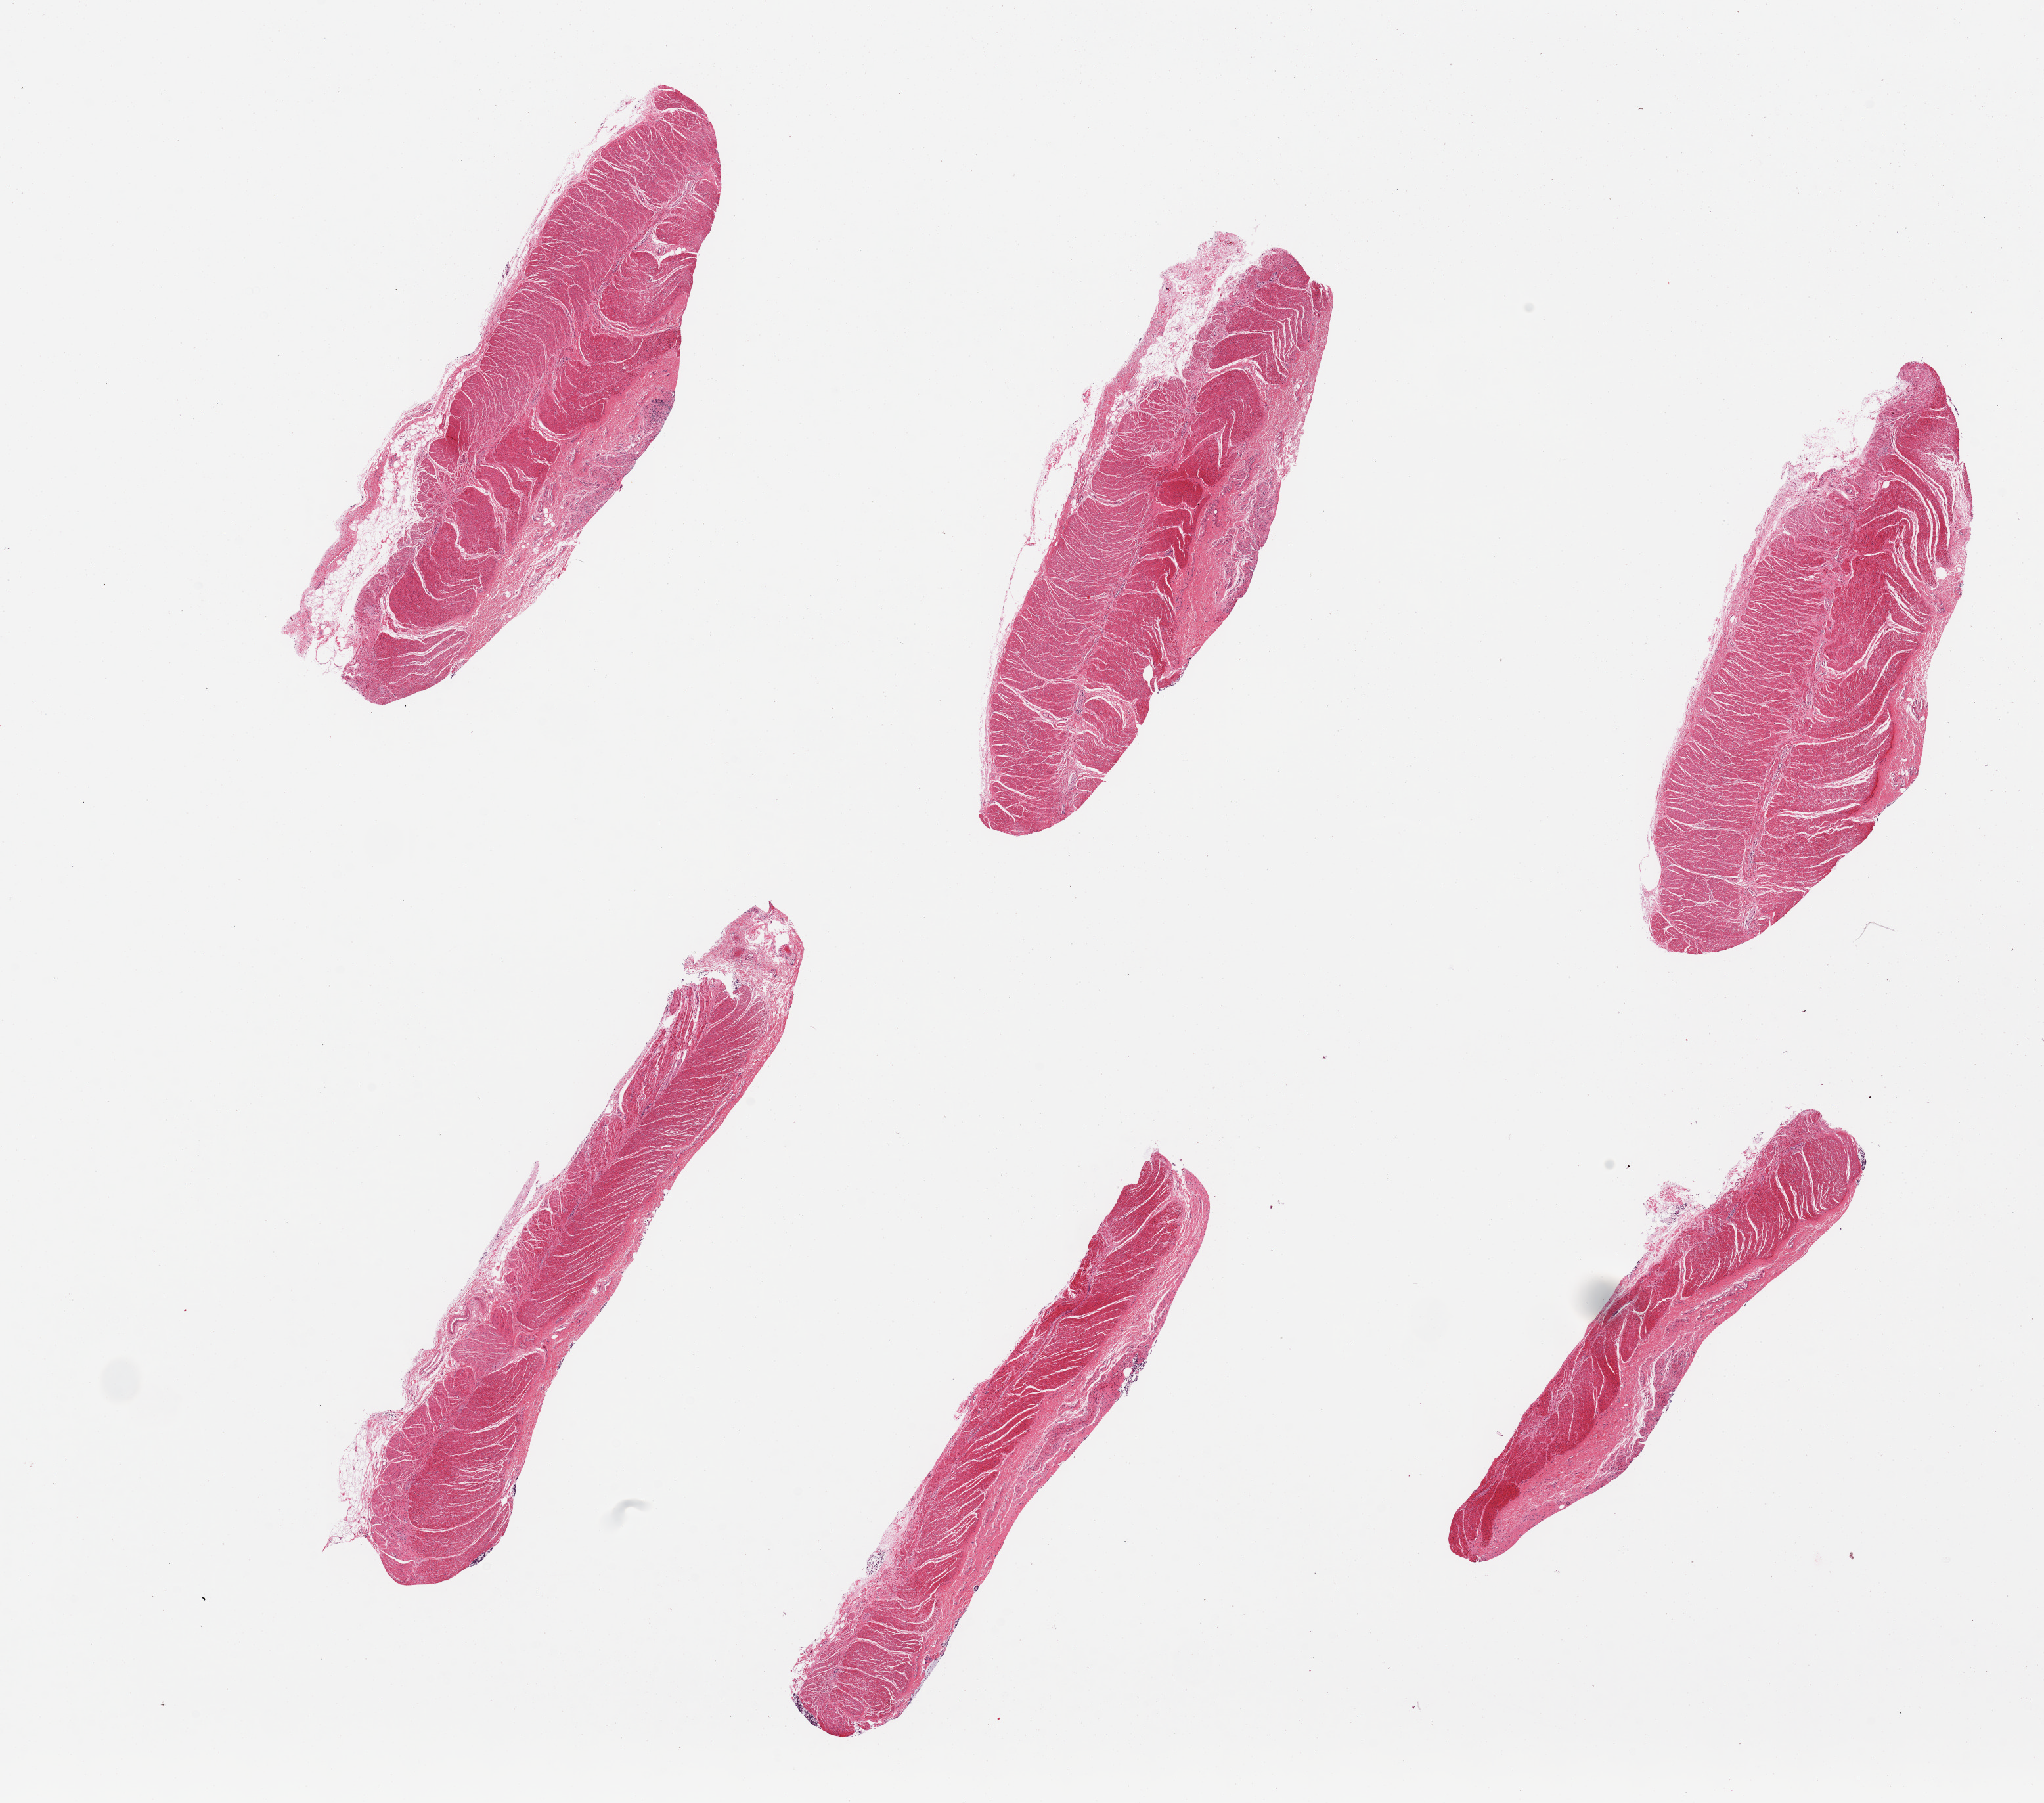
Haematoxylin and eosin whole-slide image — low-resolution overview of the scanned area, about 24.6 x 21.7 mm. PAXgene-fixed paraffin-embedded (PFPE) section. Sampled site (target tissue): sigmoid colon. Donor tissue sample. Donor: female.
- review note (as recorded): 6 pieces, all muscularis